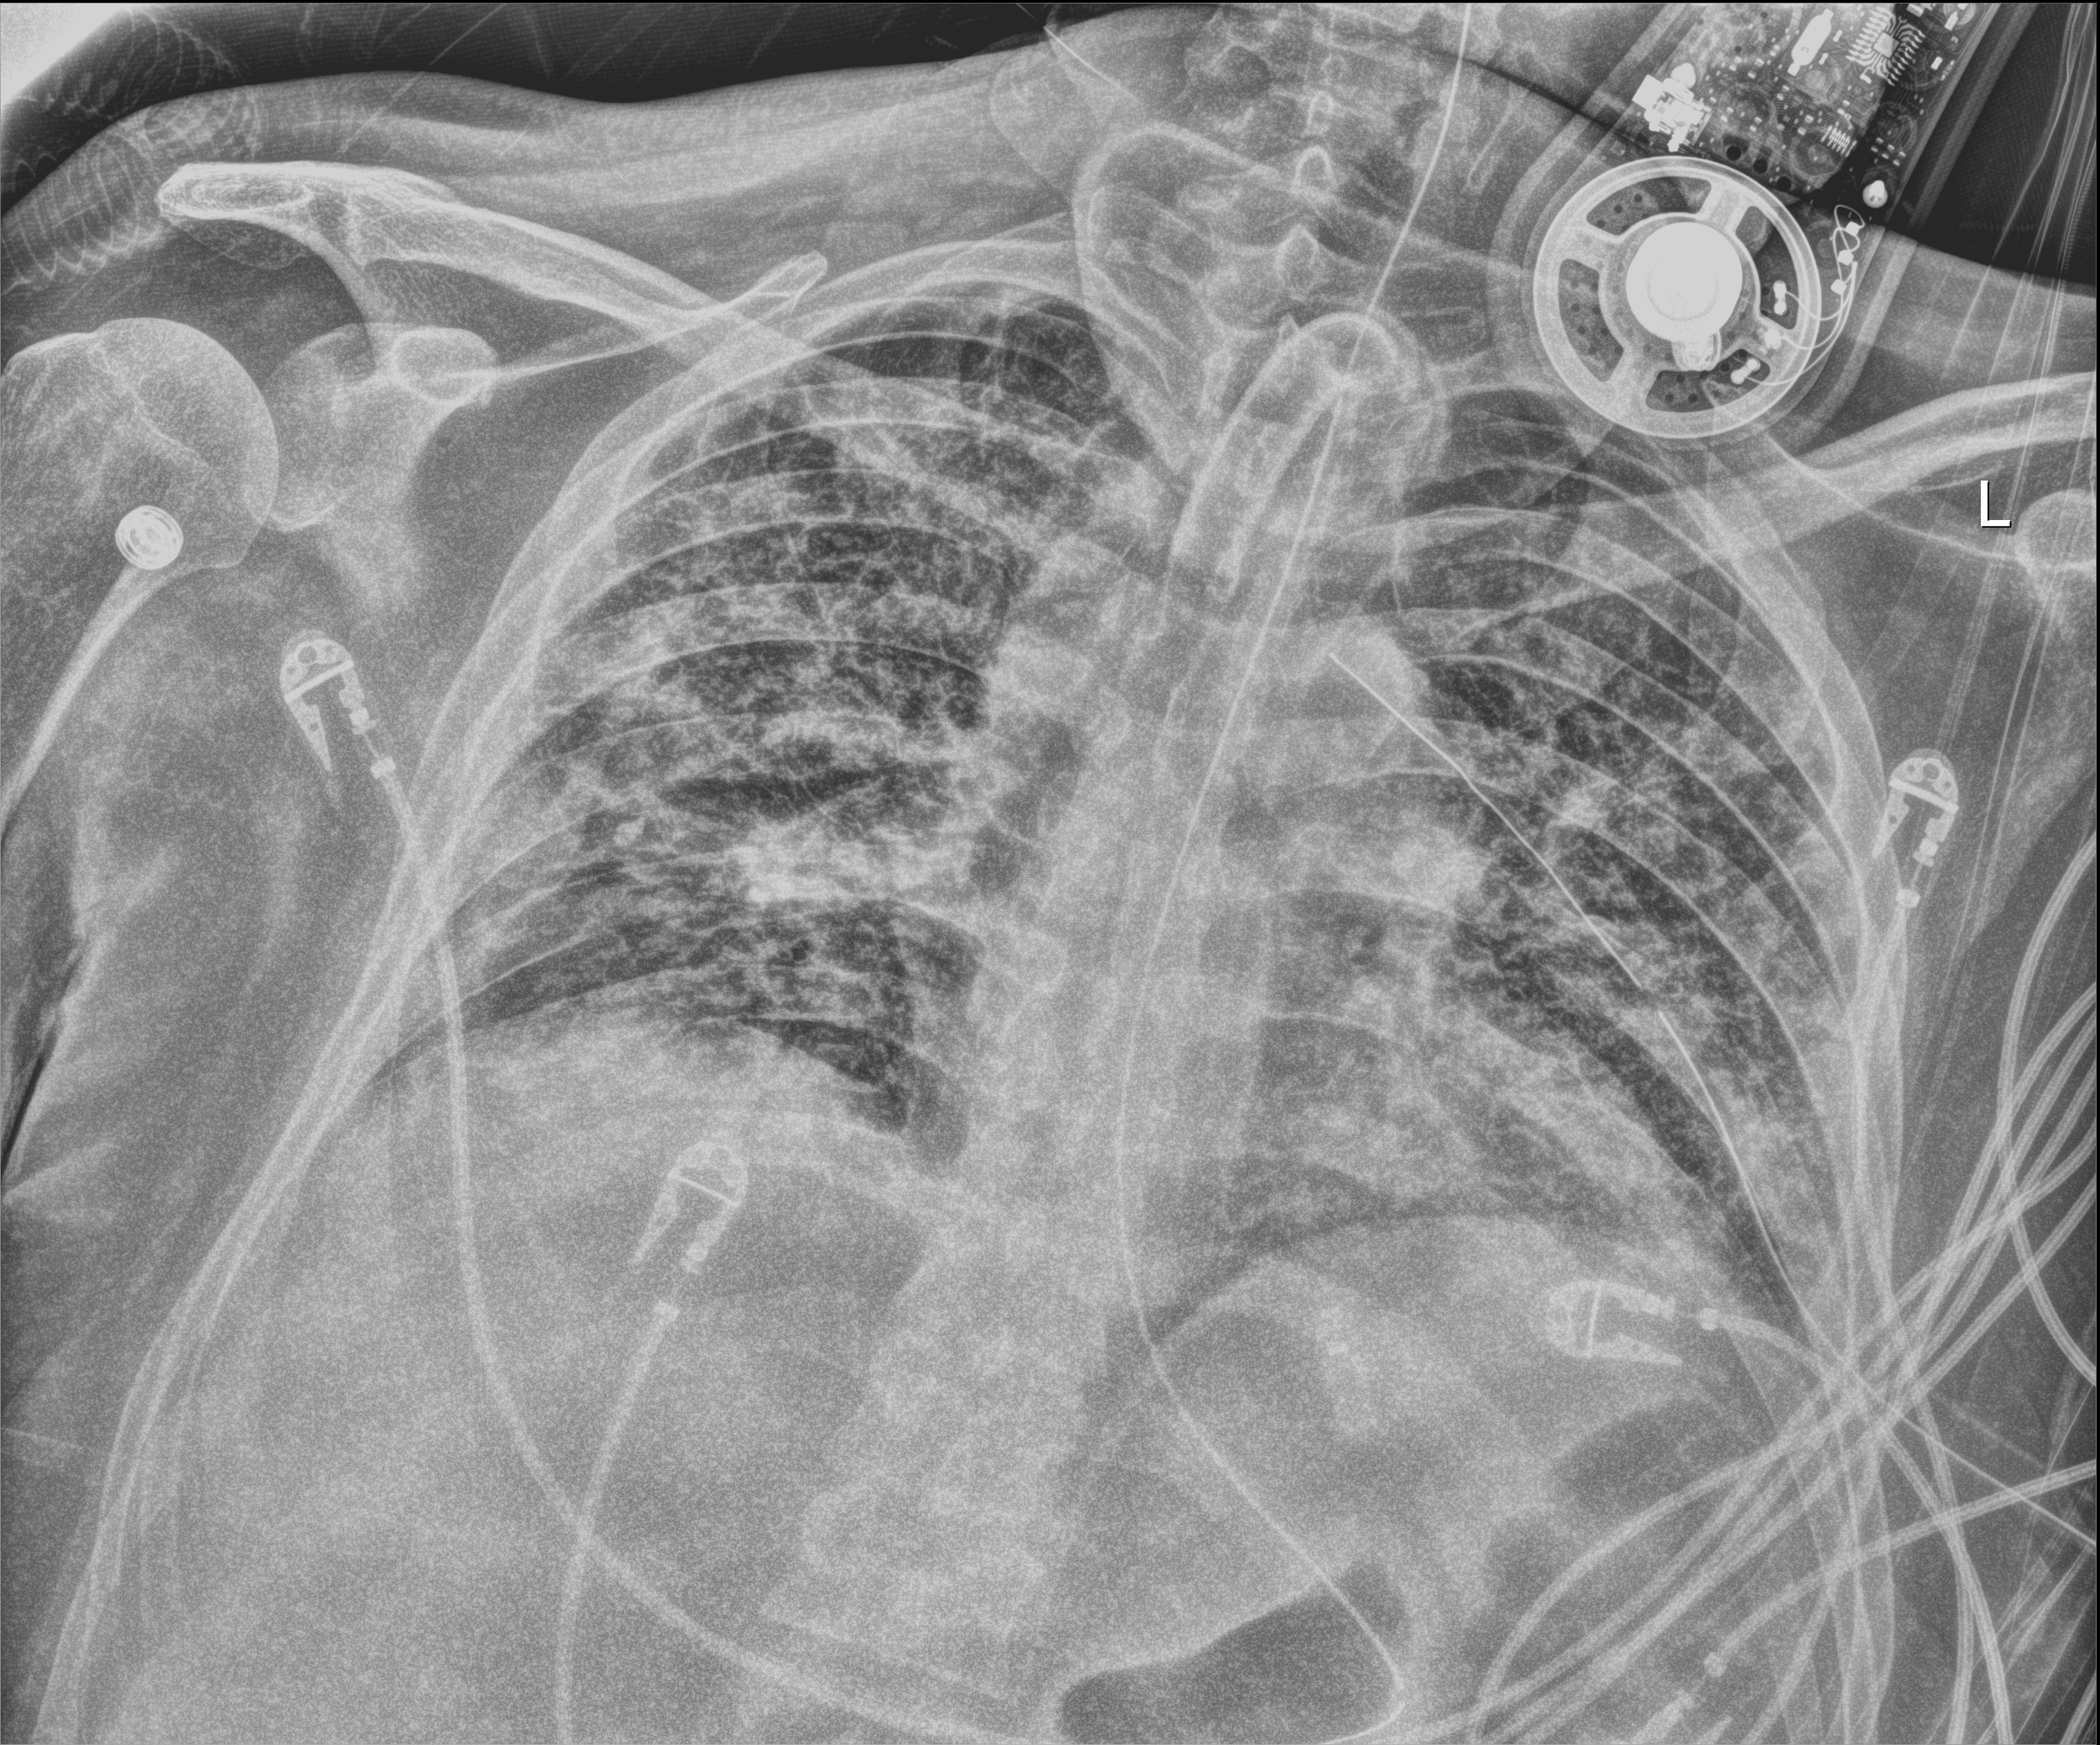
Chest X-ray; anteroposterior (AP) projection. Patient hospitalised with COVID-19; male, aged 18–59 years.
Hospital-stay facts (about this admission, not read from this image; timing relative to this image not recorded): chronic kidney disease (admission record): no; mechanically ventilated during this hospital stay: yes; other chronic lung disease (admission record): no.